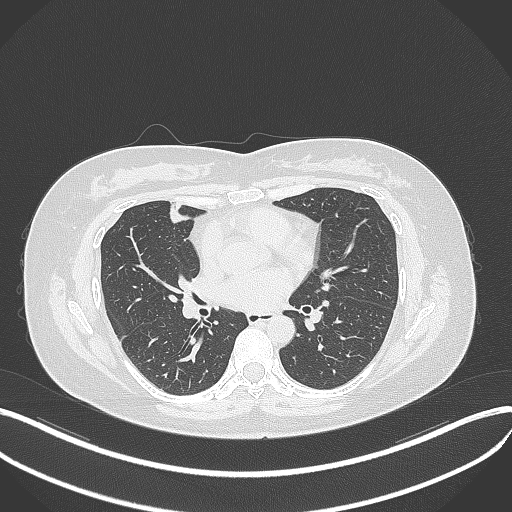
Chest CT, one axial slice; slice 158 of 273 in the series (ordered by position); 120 kVp; lung window (W 1500 / L -600 HU); 1 mm slice thickness; 512 × 512 image matrix, field of view 400 × 400 mm. Female patient, age 42 years. From the clinical record (not read from this slice): clinical TNM (as recorded): T1b N0 M0.
Outlined on this slice (rectangle marked by the reading radiologist):
- lung tumour (recorded histology: adenocarcinoma): bounding box <166,201,190,228> (left, top, right, bottom; pixels)